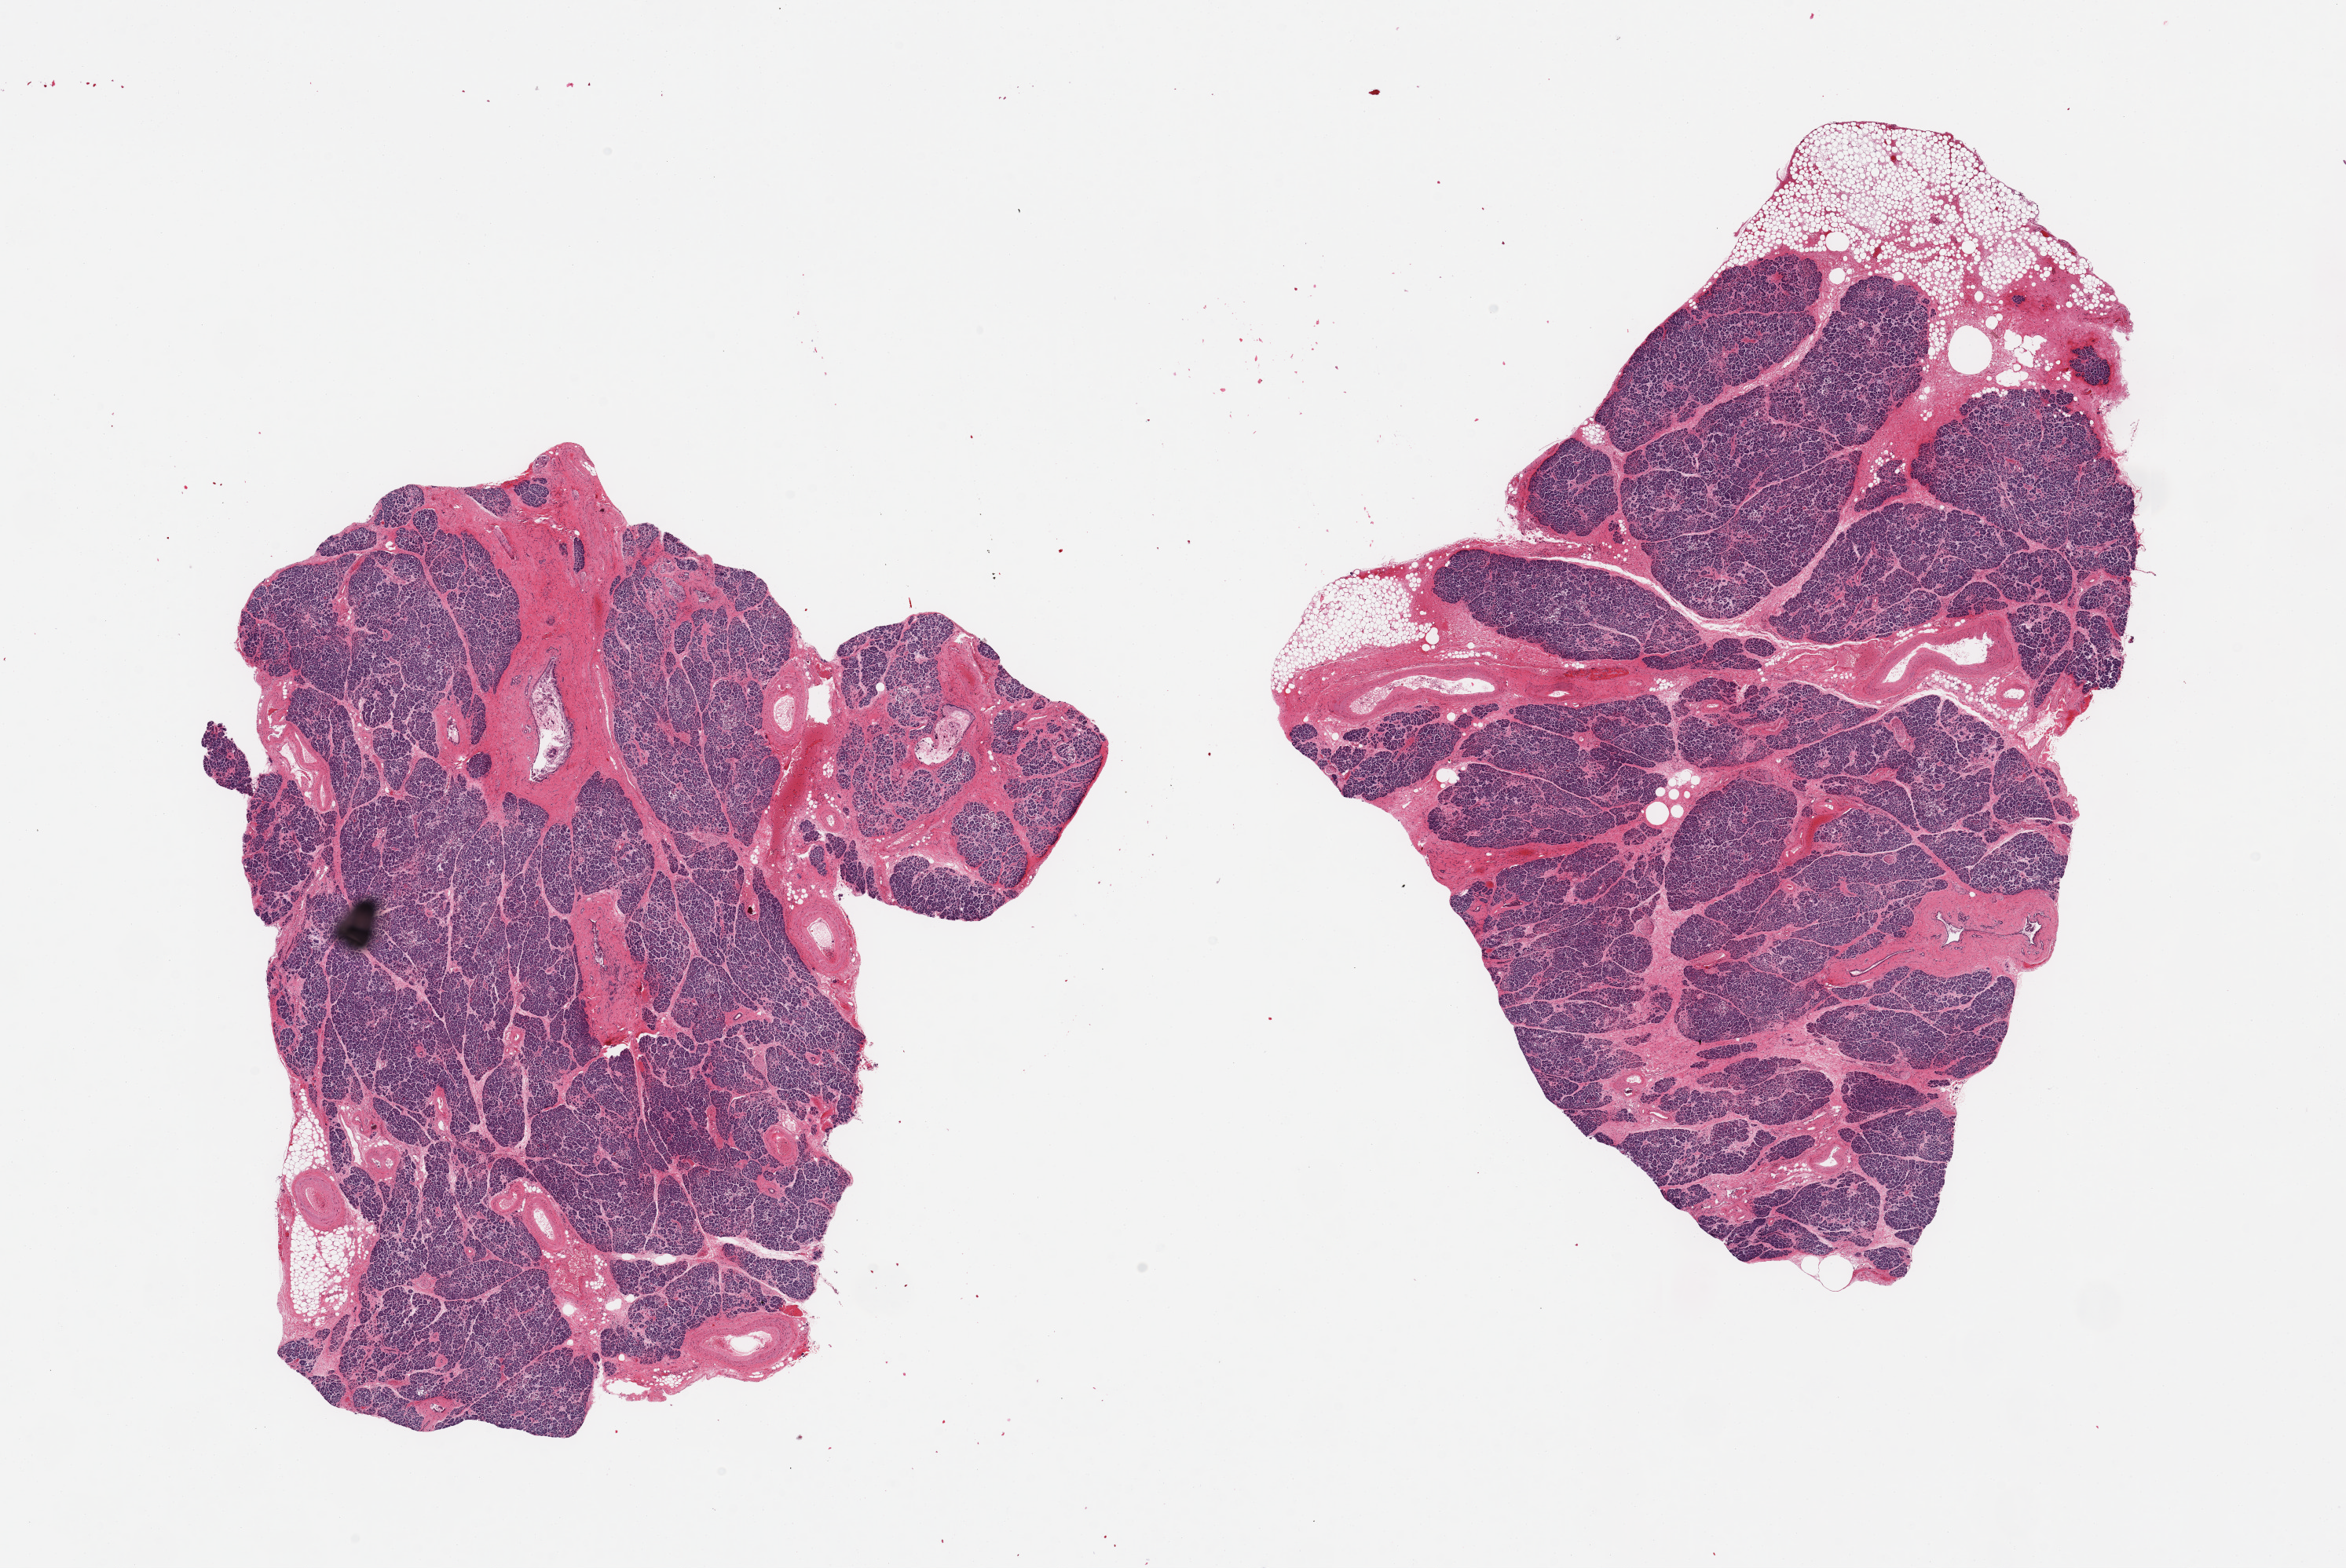
Haematoxylin and eosin whole-slide image — shown as a low-resolution overview of the whole scanned area (about 23.6 x 15.8 mm, slide scanned at 20x); PAXgene-fixed, paraffin-embedded tissue; target tissue: pancreas; donor tissue sample. Female donor.
* reviewer comment on this tissue sample: 2 pieces, moderate saponification; Islets badly preserved